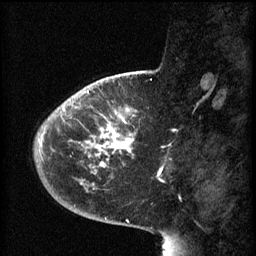
Breast MRI (dynamic contrast-enhanced), one sagittal slice. Position 17 of 60 along the scan axis. 3 images stored at this slice position (order not interpretable as contrast timing). 1.5 T. TE 4.2 ms, TR 8.1 ms. 2 mm slice thickness. 256 × 256 image matrix, field of view 200 × 200 mm. Female patient, age 44 years.
Structures marked on this image (semi-automatic segmentation, software-assisted and operator-edited):
- analysis volume of interest (the breast-tissue region the enhancement analysis was run in; not a lesion): bounding box <59,110,137,169> (left, top, right, bottom; pixels)
- tumour enhancement mask (voxels above the 70 % enhancement threshold inside the analysis volume of interest): <60,110,134,167>